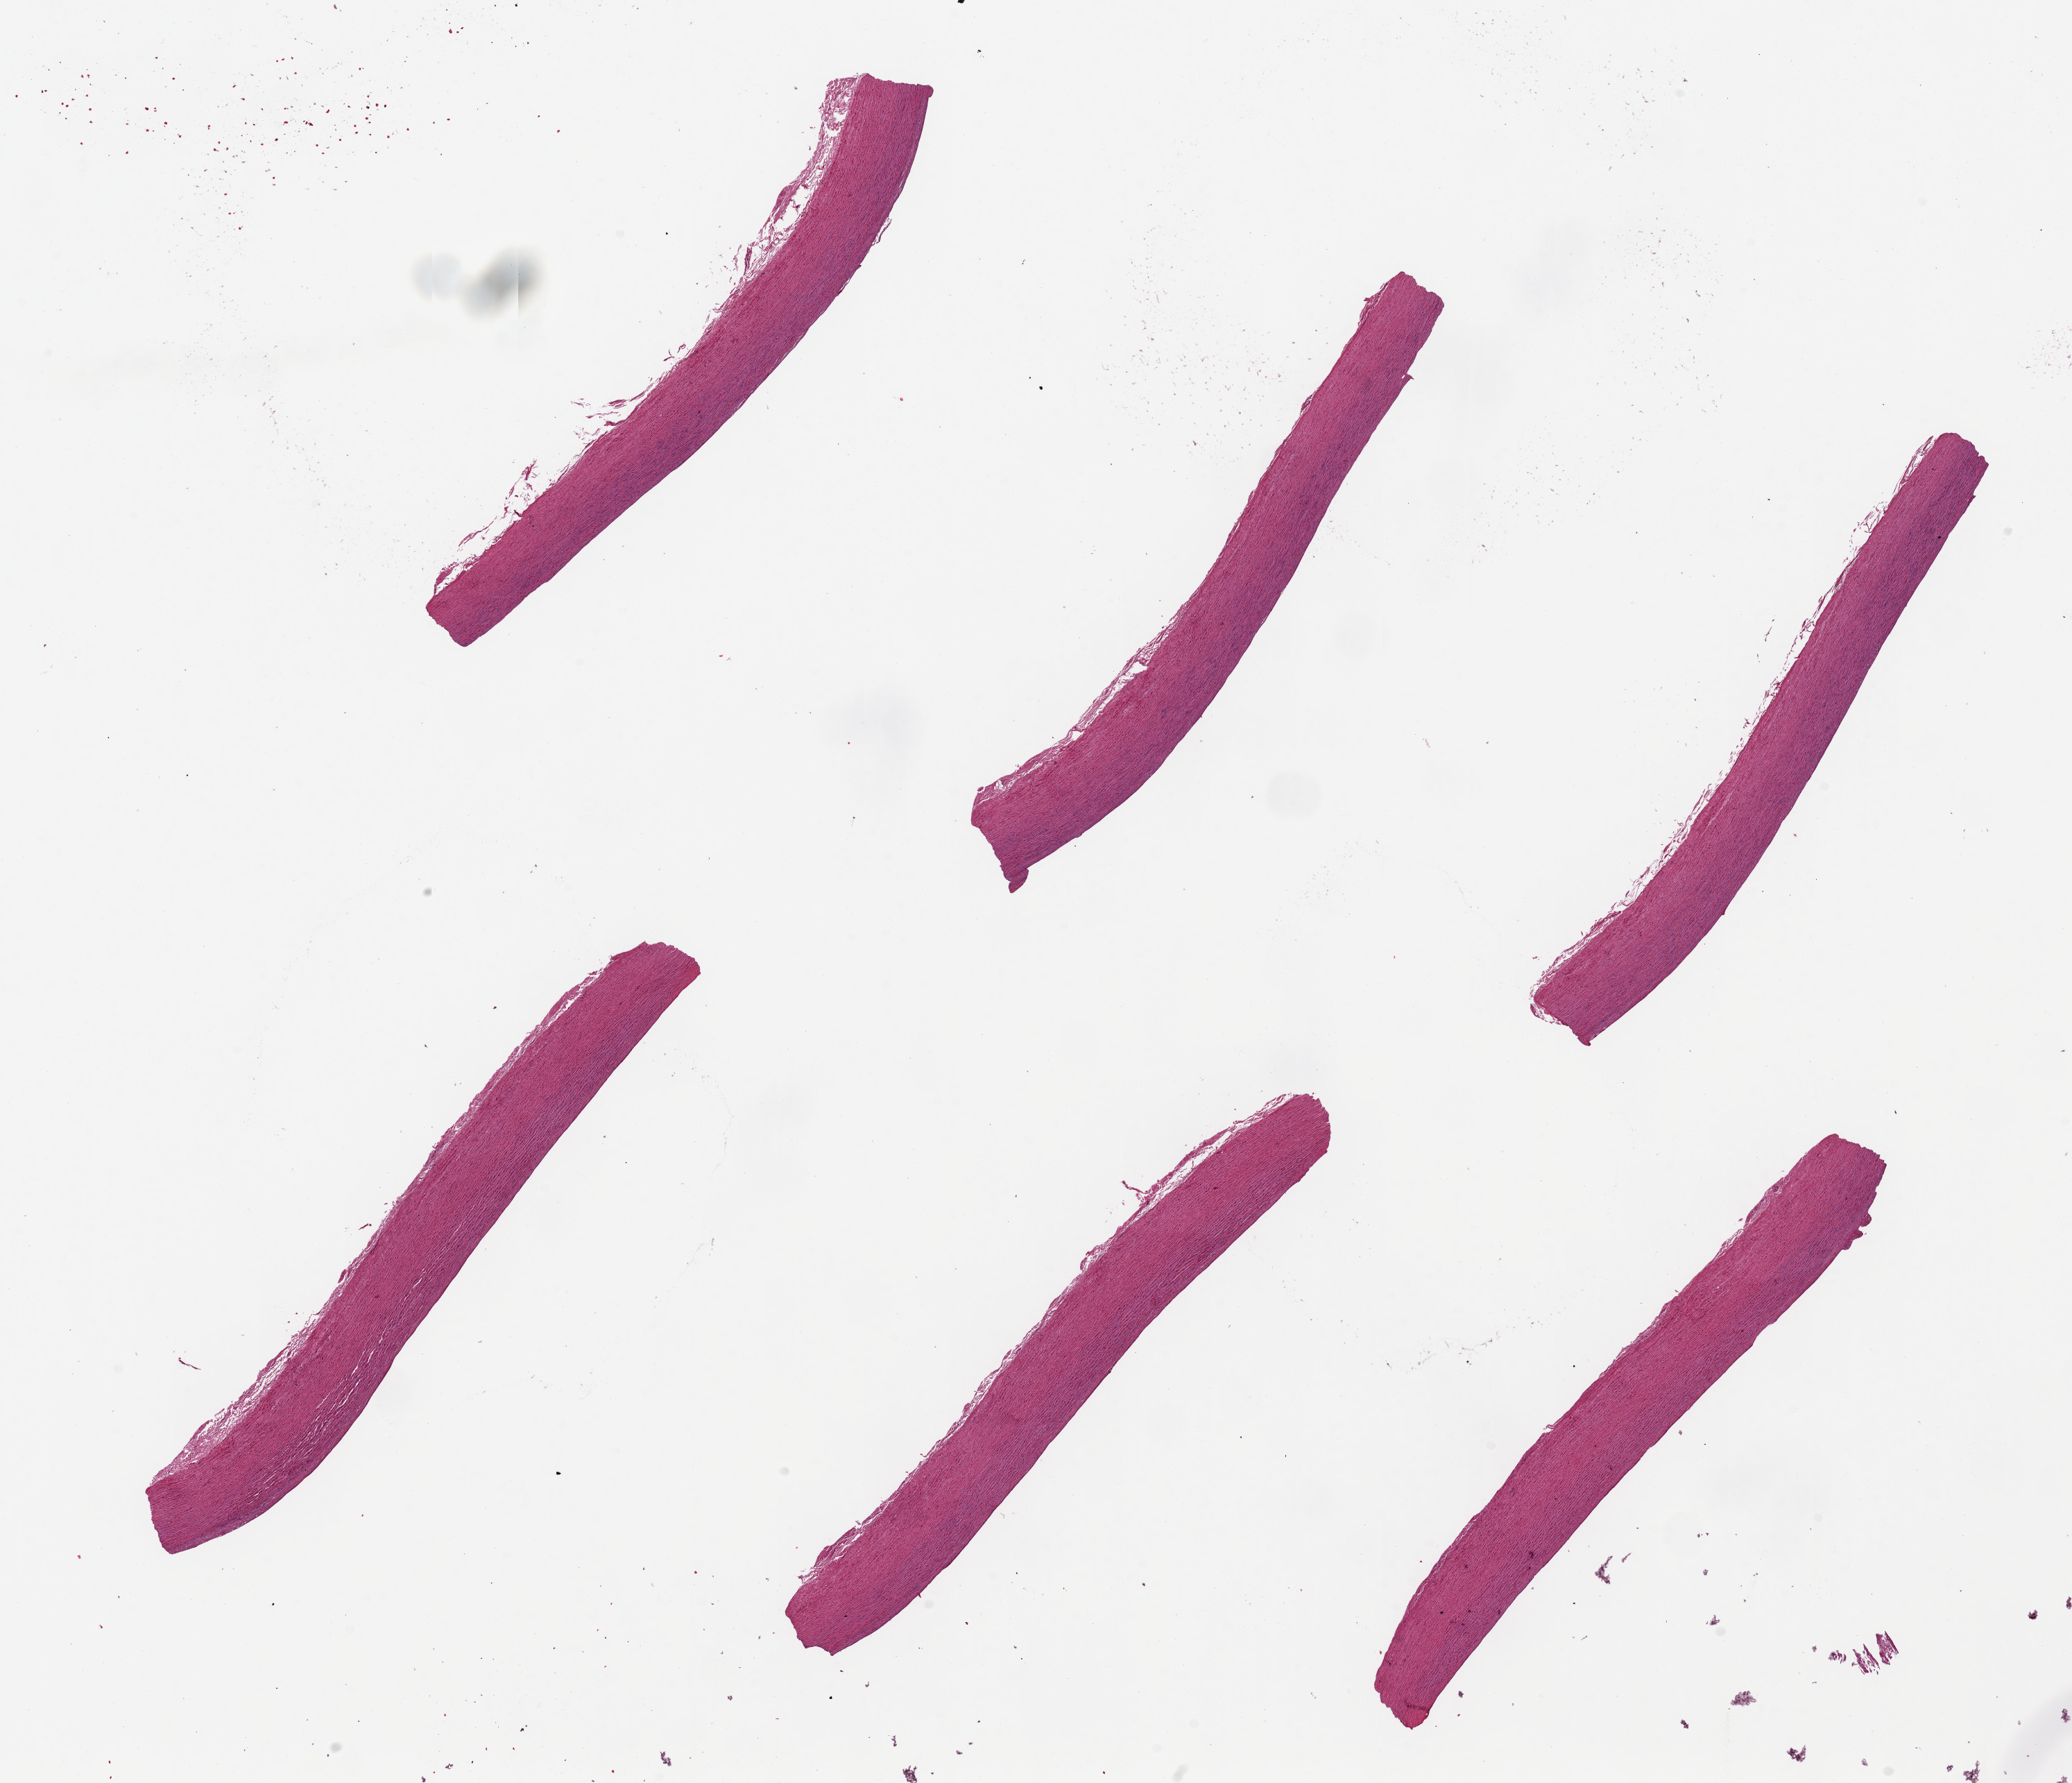
Whole-slide image, hematoxylin and eosin (H&E) stain, whole scanned area (about 23.6 x 20.3 mm) shown as a low-resolution overview; PAXgene-fixed, paraffin-embedded tissue; sampled site (target tissue): aorta; donor tissue sample. Donor: female.
* review note (as recorded): 6 pieces, ~8x1mm, no visible atherosclerosis